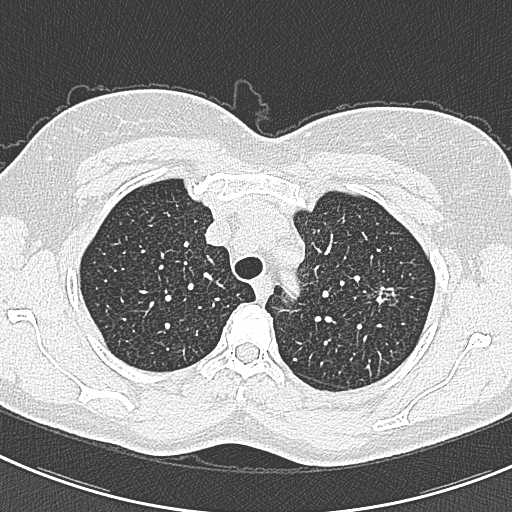
Chest CT (low-dose screening protocol), one axial image. Baseline screening round. Lung window (W 1500 / L -600 HU). 1 mm slice thickness. Slice 59 of 309 in the series. Female, age 57 years at enrolment. Current smoker at enrolment.
Expert reader's lesion annotation, box from (x=362, y=276) to (x=413, y=321) px. The screening reader recorded 2 non-calcified nodules or masses ≥4 mm on this exam; which of them this box marks is not recorded.